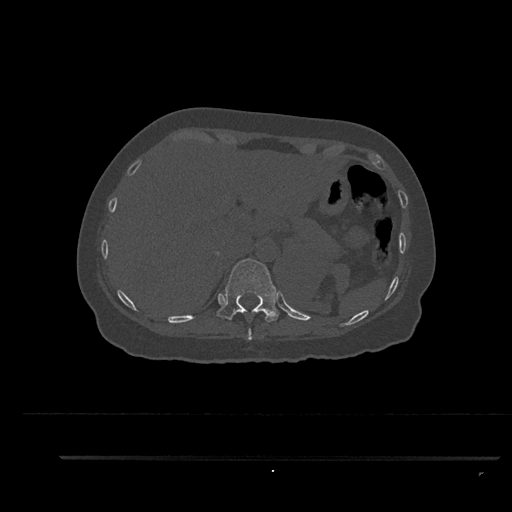
CT including the spine, one axial slice; slice 326 of 797 in the series (ordered by position); reconstruction kernel Br40s/3; 120 kVp; bone window (W 1800 / L 400 HU); 0.5 mm slice thickness; 512 × 512 image matrix, field of view 408 × 408 mm. Patient: female, 44 years. From the clinical record (not read from this slice): primary cancer: renal; vertebrae with lytic lesions (as recorded): L1.
Structures marked on this image (semi-automatic segmentation, software-assisted and operator-edited):
- T10 vertebra: bounding box (x1, y1, x2, y2) in pixels: (247, 311, 252, 340)
- T11 vertebra: (216, 259, 280, 322)